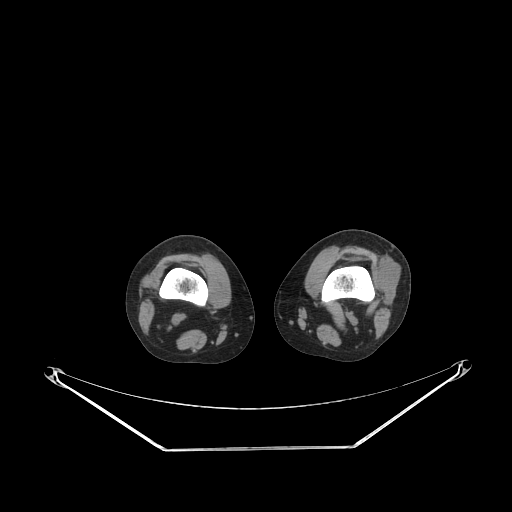
CT of an extremity soft-tissue mass (from a PET/CT study), one axial slice; slice 170 of 223 in the series (ordered by position); soft-tissue window (W 400 / L 40 HU); 3.75 mm slice thickness; 512 × 512 image matrix, field of view 500 × 500 mm. Female patient. Case-level facts recorded for this patient, not image findings: histological type: spindle cell suggestive of biphasic synovial sarcoma; grade: intermediate; site of the primary tumour: left knee.
Outlined on this slice (expert contour drawn on MRI and transferred to this co-registered scan by the dataset authors):
- gross tumour volume including surrounding oedema: box from (x=374, y=254) to (x=398, y=303) px
- gross tumour volume (mass): (x=374, y=256)–(x=398, y=303)